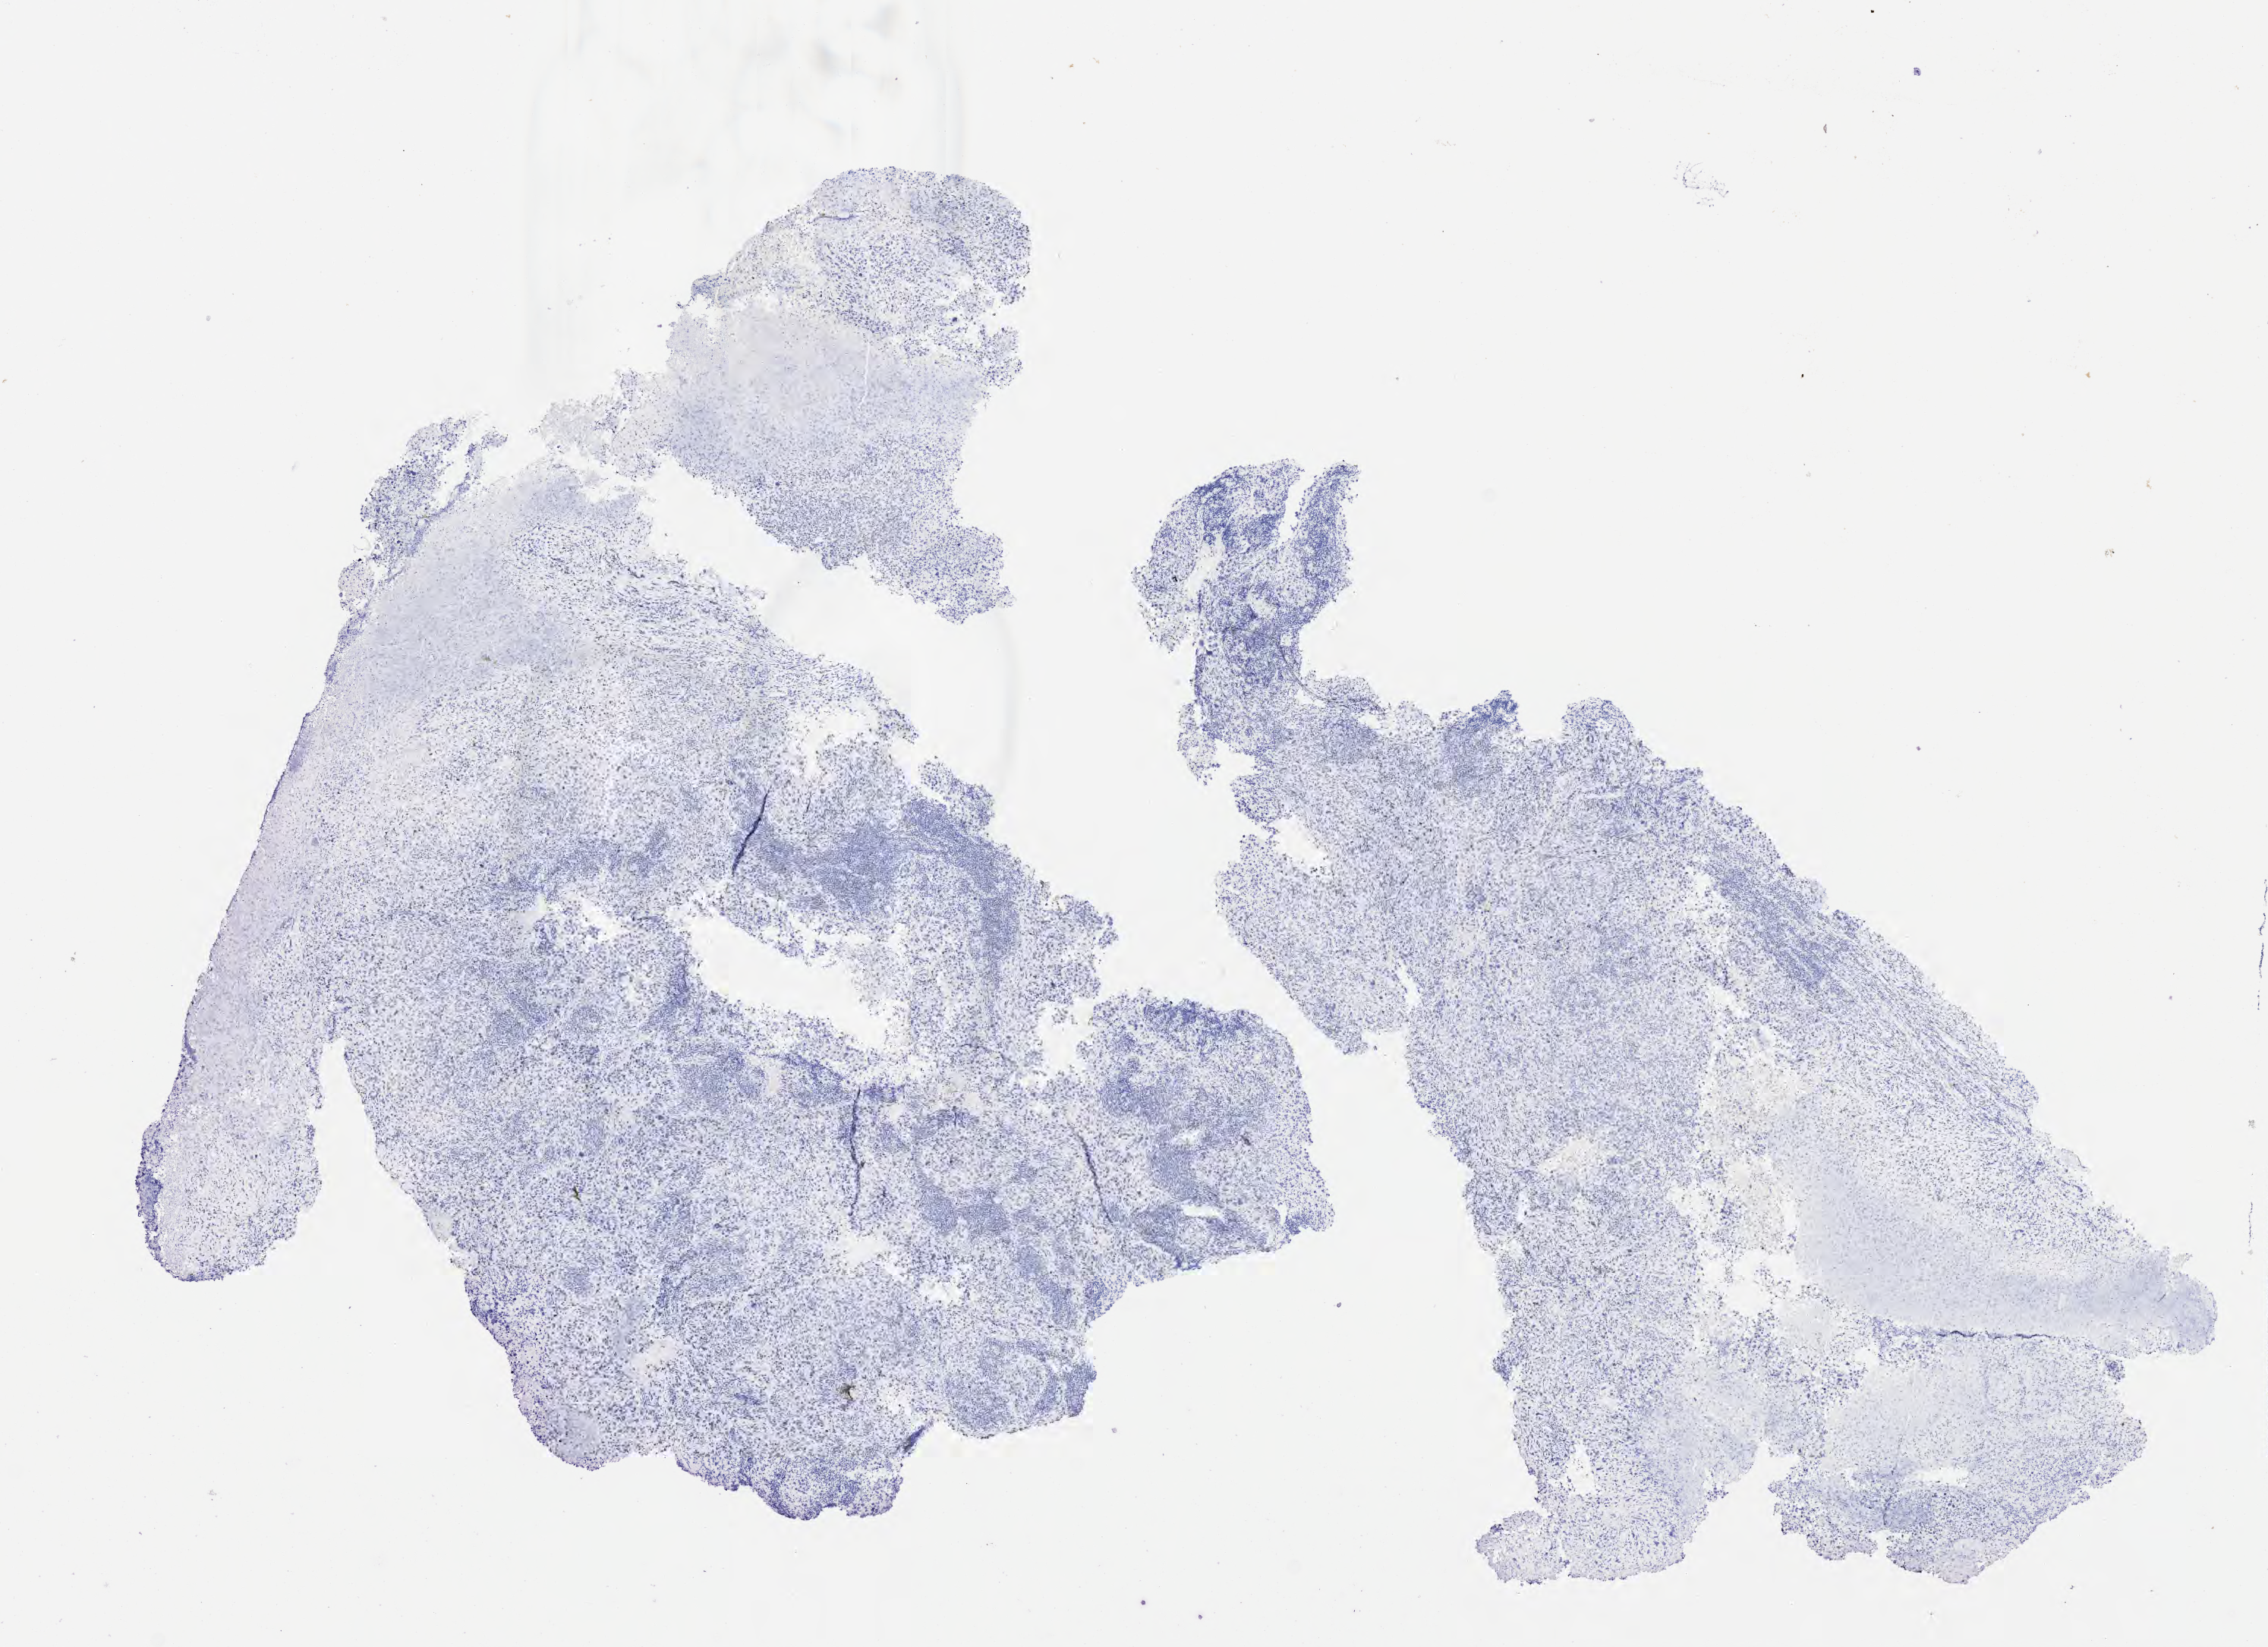
Whole-slide image, immunohistochemical stain for p40 — low-resolution overview of the scanned area, about 12.1 x 8.8 mm; tumor tissue; site: cervix. Female patient, 38 years old.
• diagnosis: Squamous cell carcinoma, large cell, nonkeratinizing, NOS